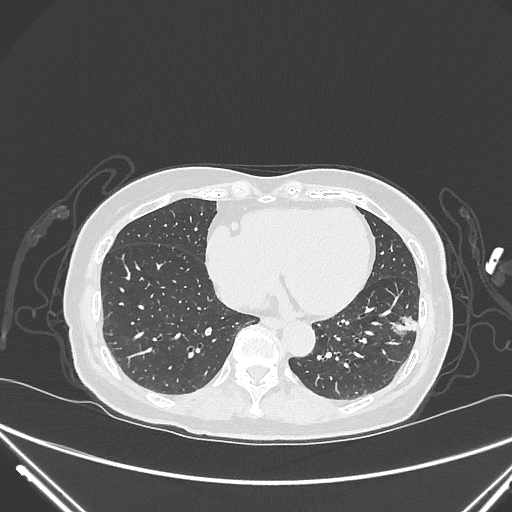
Chest CT, one axial slice. Slice 104 of 310 in the series (ordered by position). 120 kVp. Lung window (W 1500 / L -600 HU). 512 × 512 image matrix. Female patient, age 82 years. From the clinical record (not read from this slice): clinical TNM (as recorded): T1c N0 M0; histopathological grade: G2.
Annotated regions visible in this slice (bounding box drawn by a radiologist):
- lung tumour (recorded histology: adenocarcinoma): box from (x=391, y=311) to (x=430, y=347) px